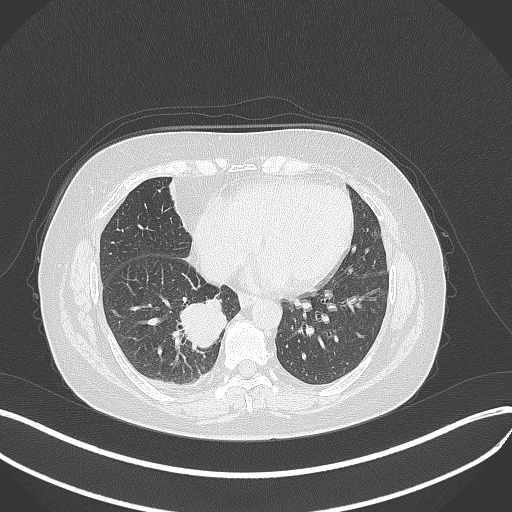
Chest CT, one axial slice. Position 130 of 381 along the scan axis. Reconstruction kernel B70f. 120 kVp. Lung window (W 1500 / L -600 HU). 1 mm slice thickness. 512 × 512 image matrix. Female patient, age 56 years. From the clinical record (not read from this slice): clinical TNM (as recorded): T2b N1 M0; histopathological grade: G3.
Annotated regions visible in this slice (rectangle marked by the reading radiologist):
- lung tumour (recorded histology: small cell carcinoma): bounding box <176,296,232,353> (left, top, right, bottom; pixels)